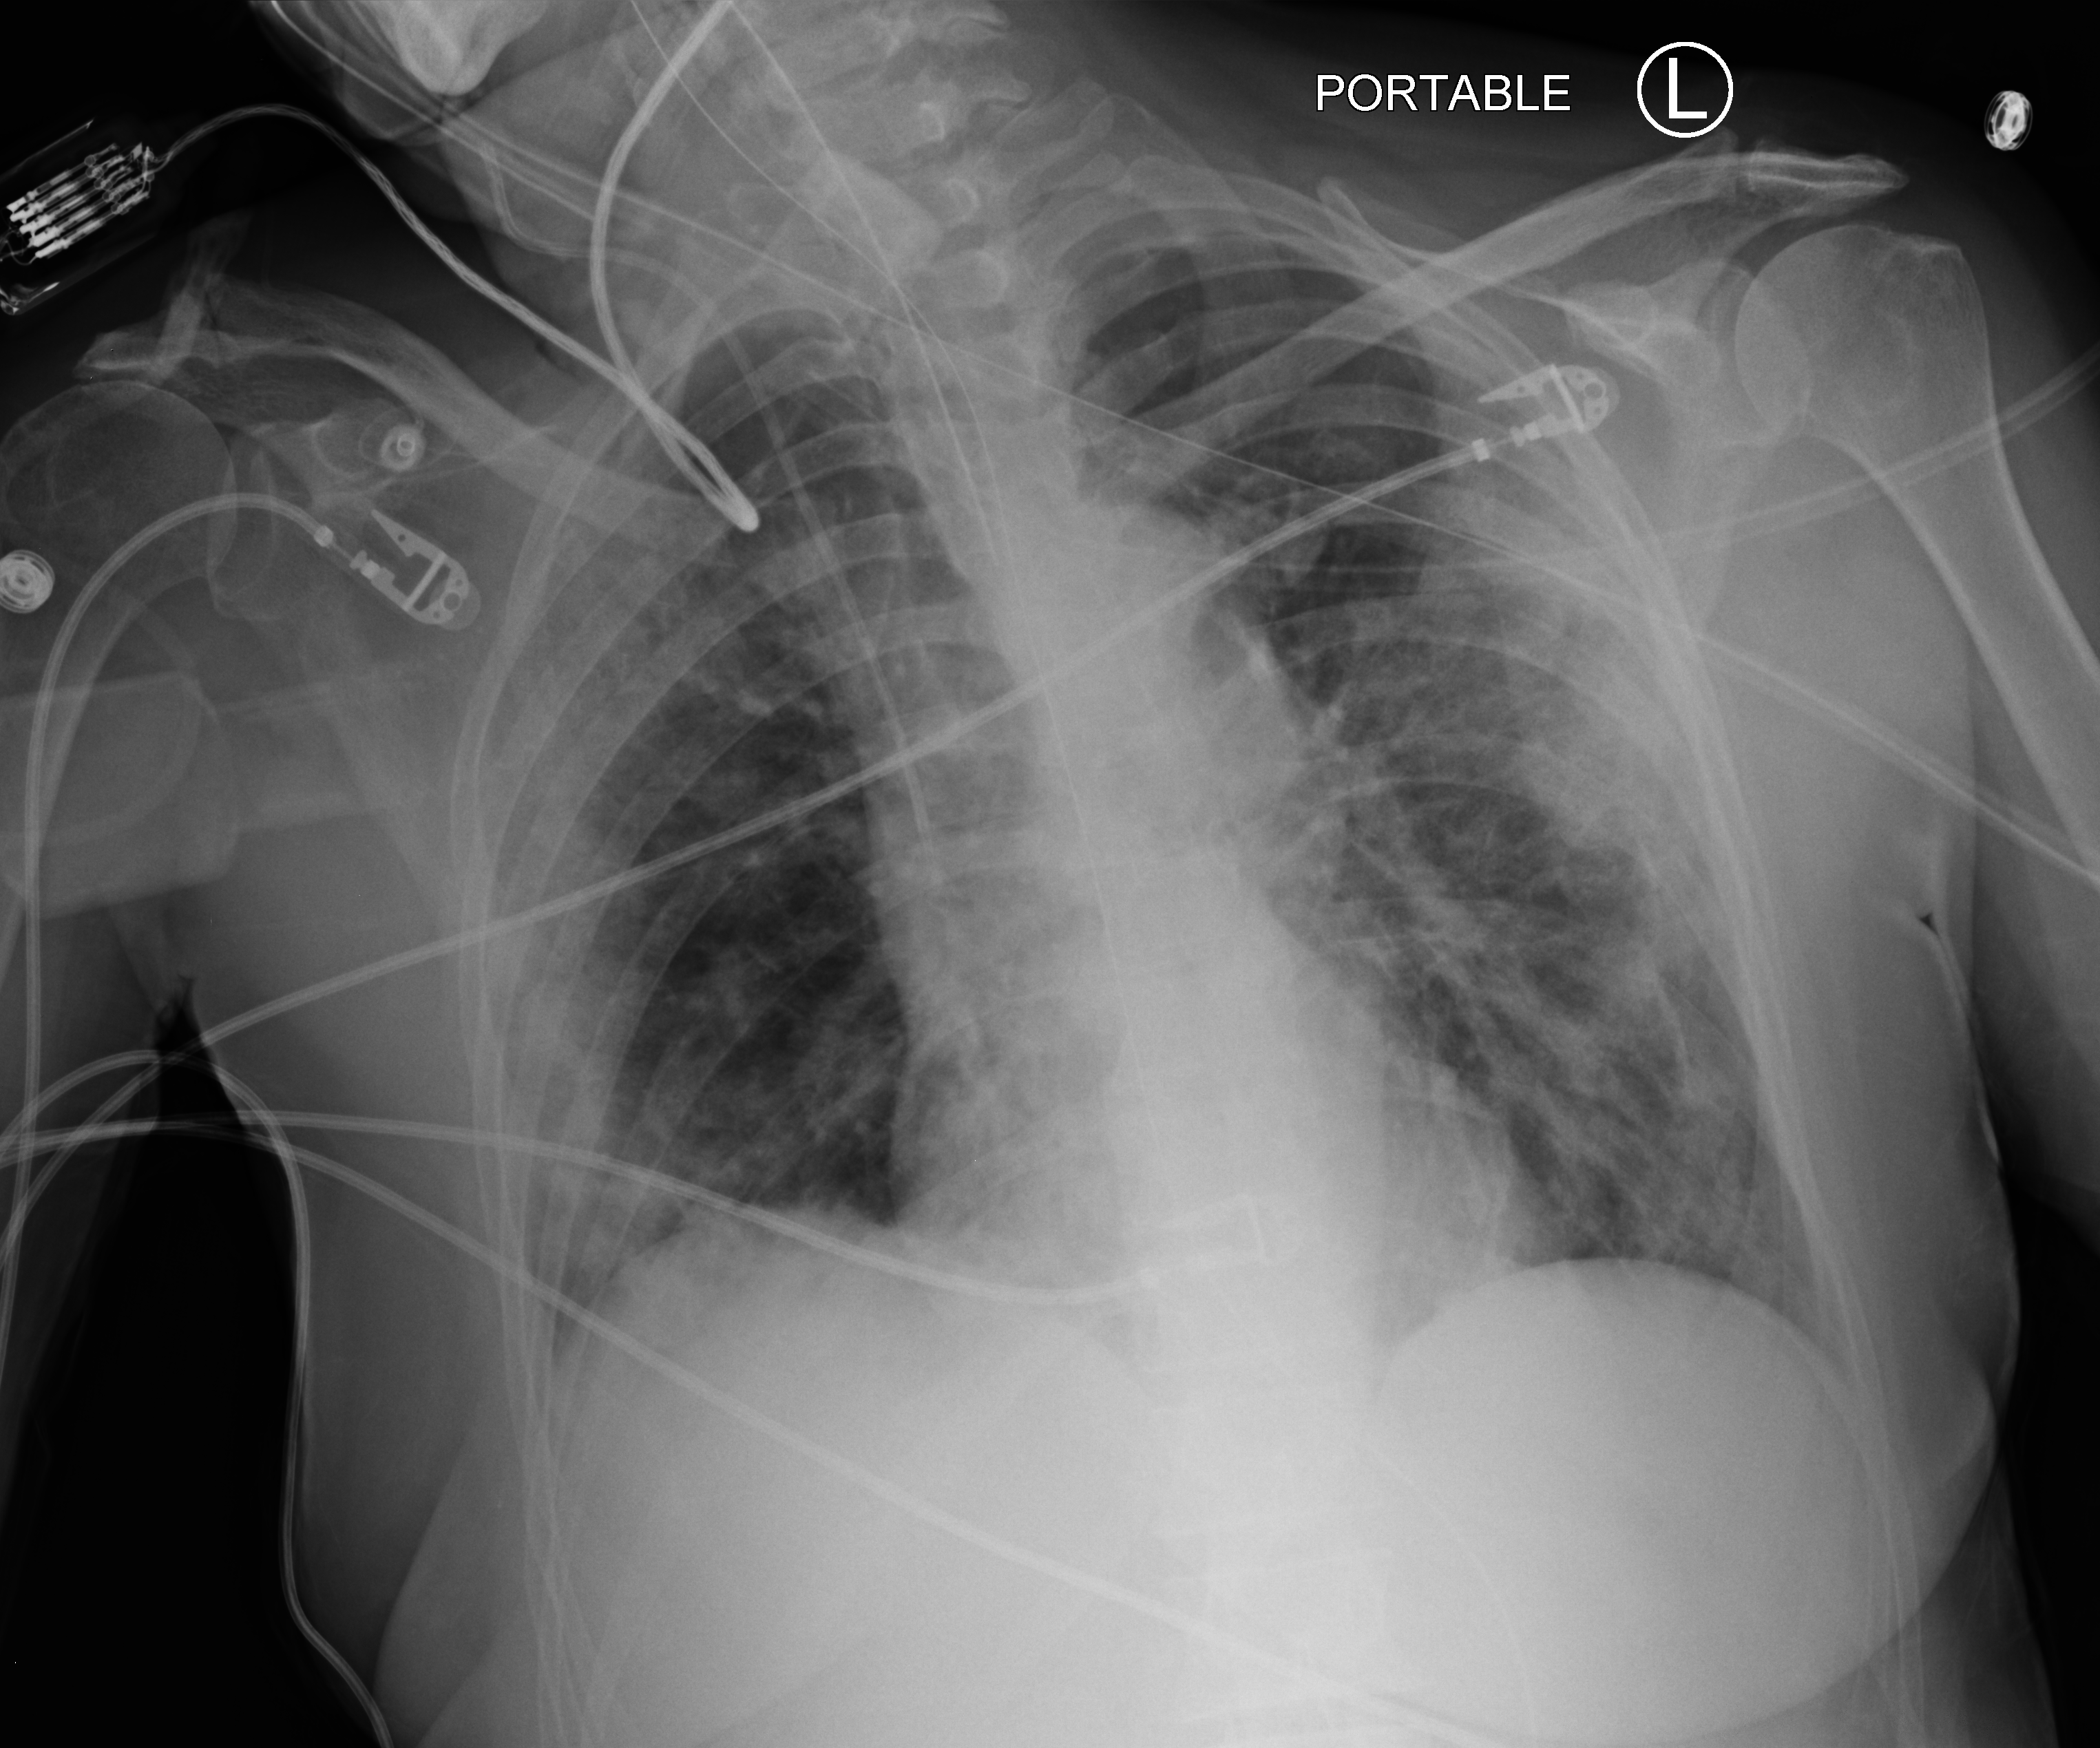
Chest X-ray (portable); anteroposterior (AP) projection. Patient hospitalised with COVID-19; female, aged 60–74 years.
Hospital-stay facts (about this admission, not read from this image; timing relative to this image not recorded): other chronic lung disease (admission record): no; diabetes (admission record): no.